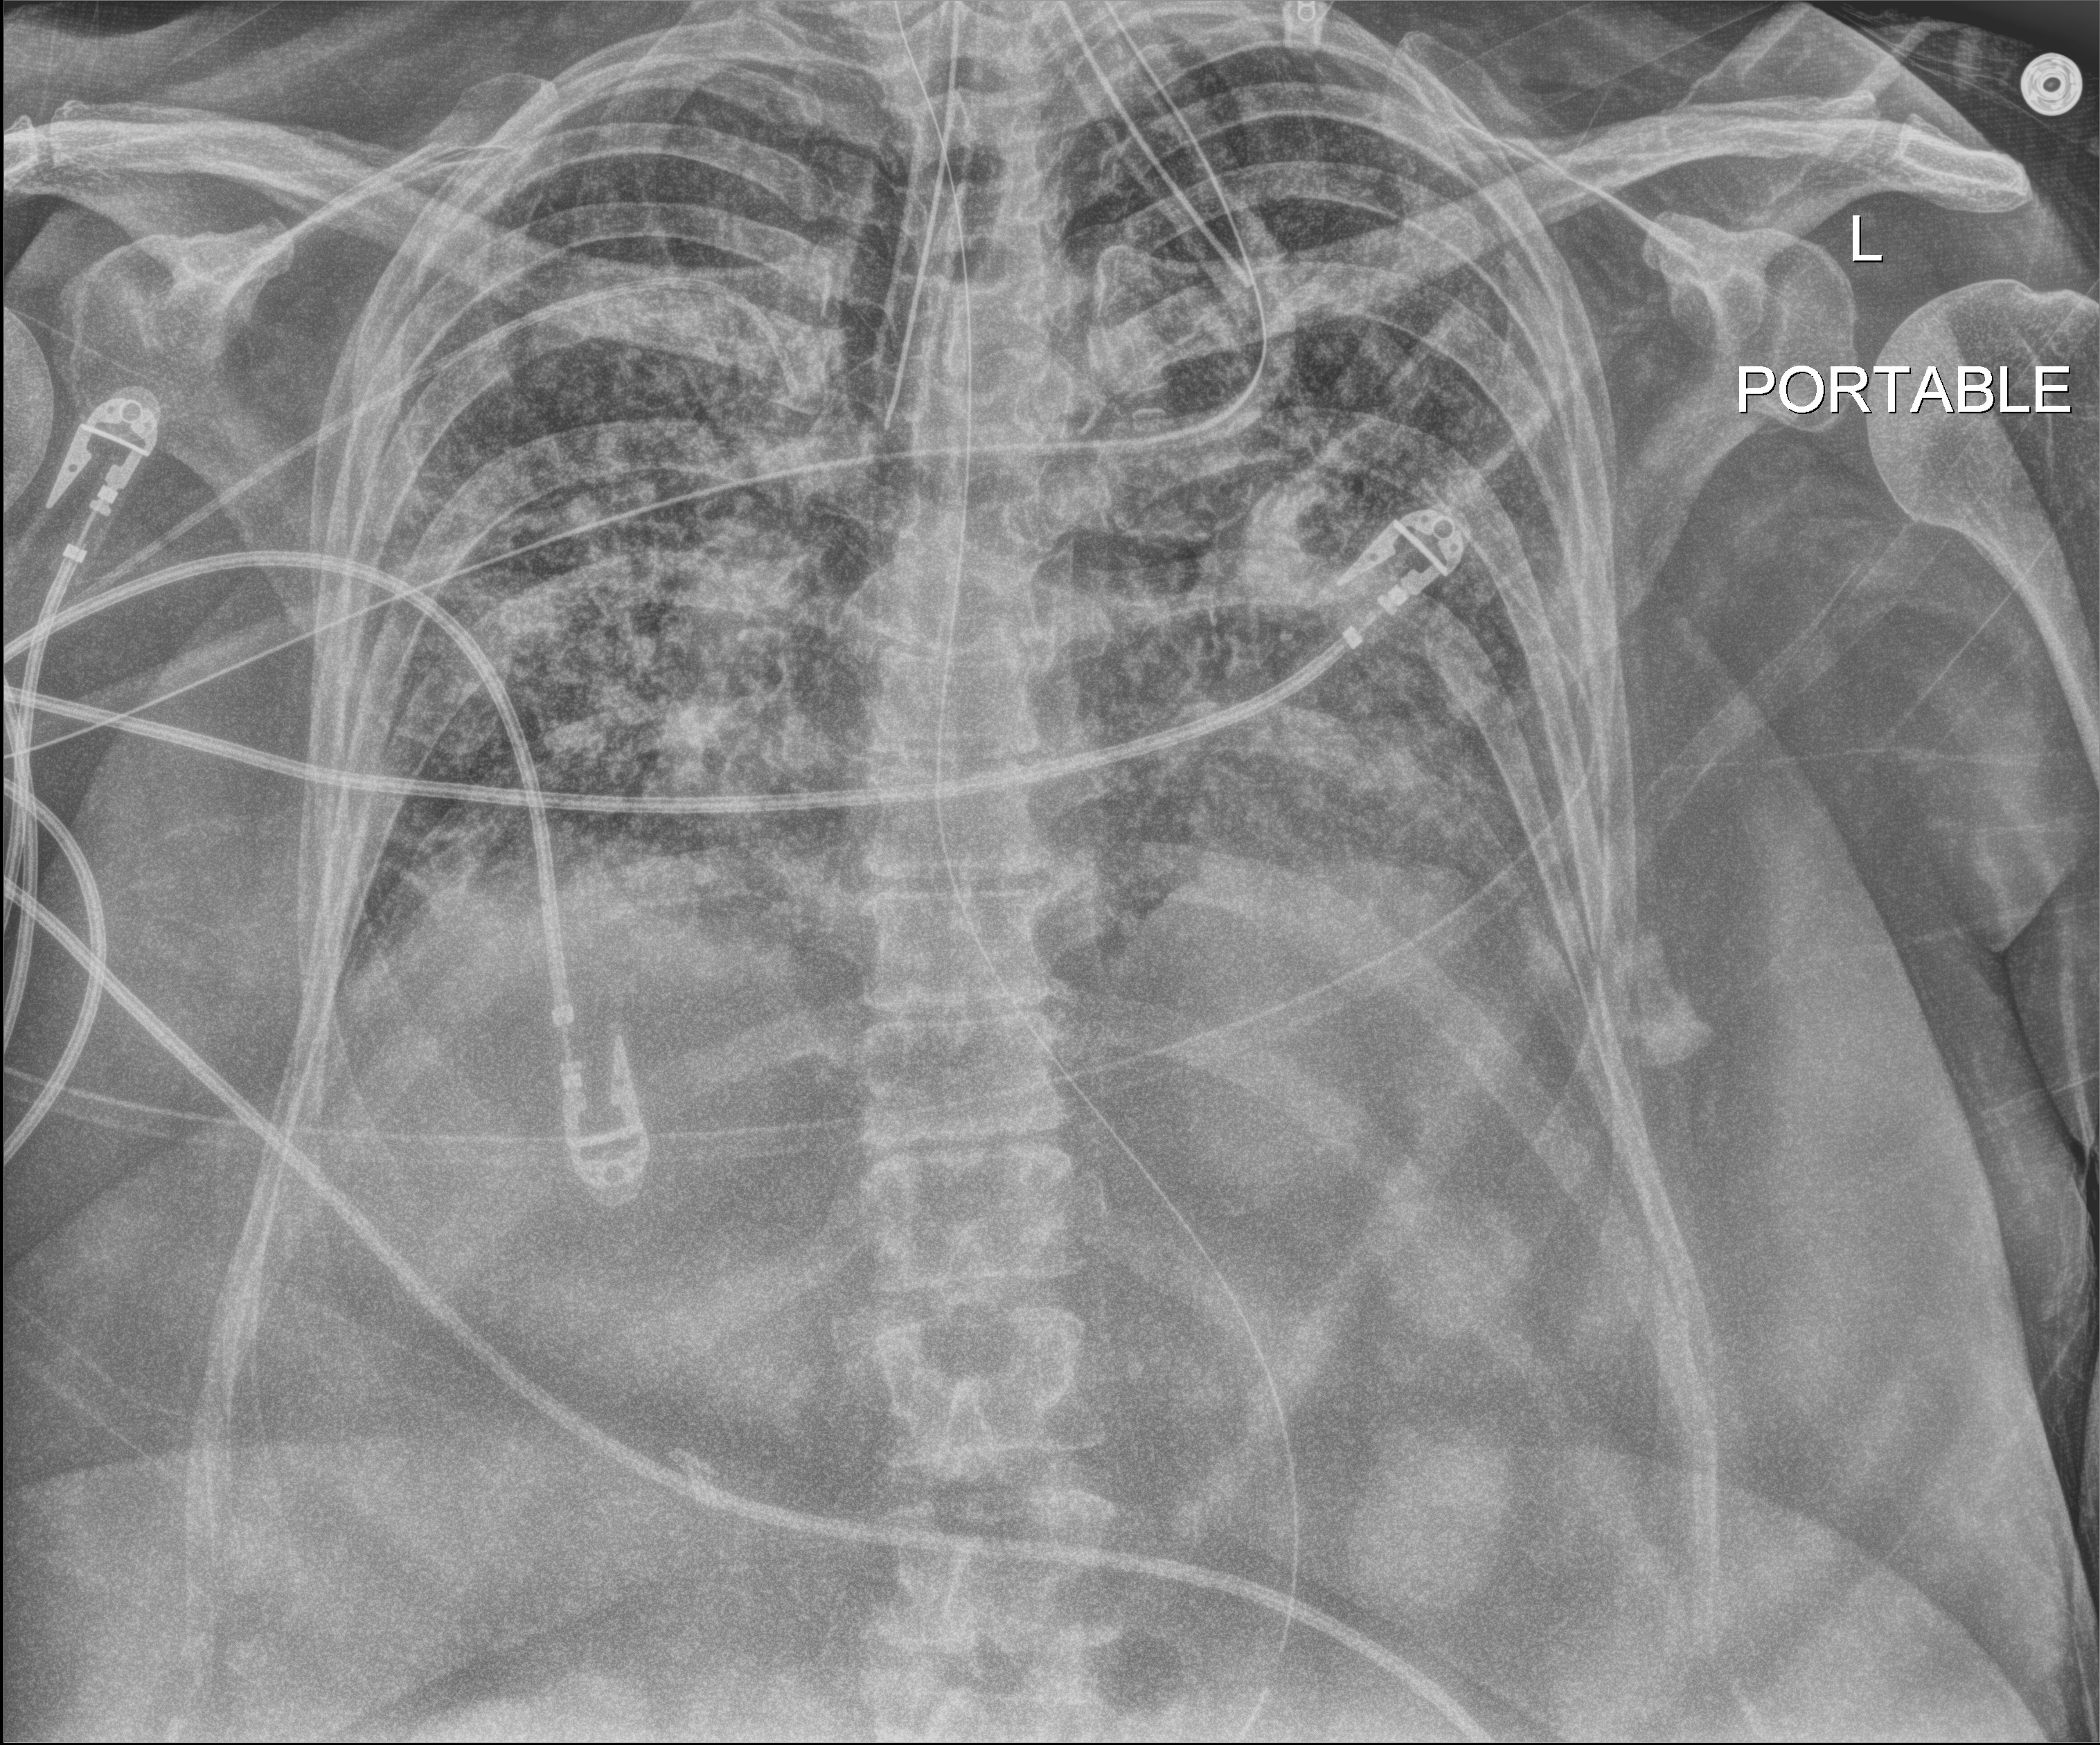
Chest X-ray (portable), anteroposterior (AP) projection. Female patient hospitalised with COVID-19, age 60–74 years.
From the hospital-stay record, not from the radiograph (when in the stay this image was taken is not recorded): chronic kidney disease (admission record): no.